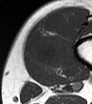
MRI of an extremity soft-tissue mass, one axial slice; position 11 of 62 along the scan axis; MR volume resampled by the dataset authors to the PET/CT grid (not the native acquisition matrix); 3.27 mm slice thickness; 92 × 104 image matrix. Male patient. From the clinical record (not read from this slice): histological type: mixoid liposarcoma; grade: low; site of the primary tumour: left thigh.
Structures marked on this image (expert contour drawn on MRI and transferred to this co-registered scan by the dataset authors):
- gross tumour volume (mass): bounding box [x1, y1, x2, y2] px = [39, 45, 58, 64]